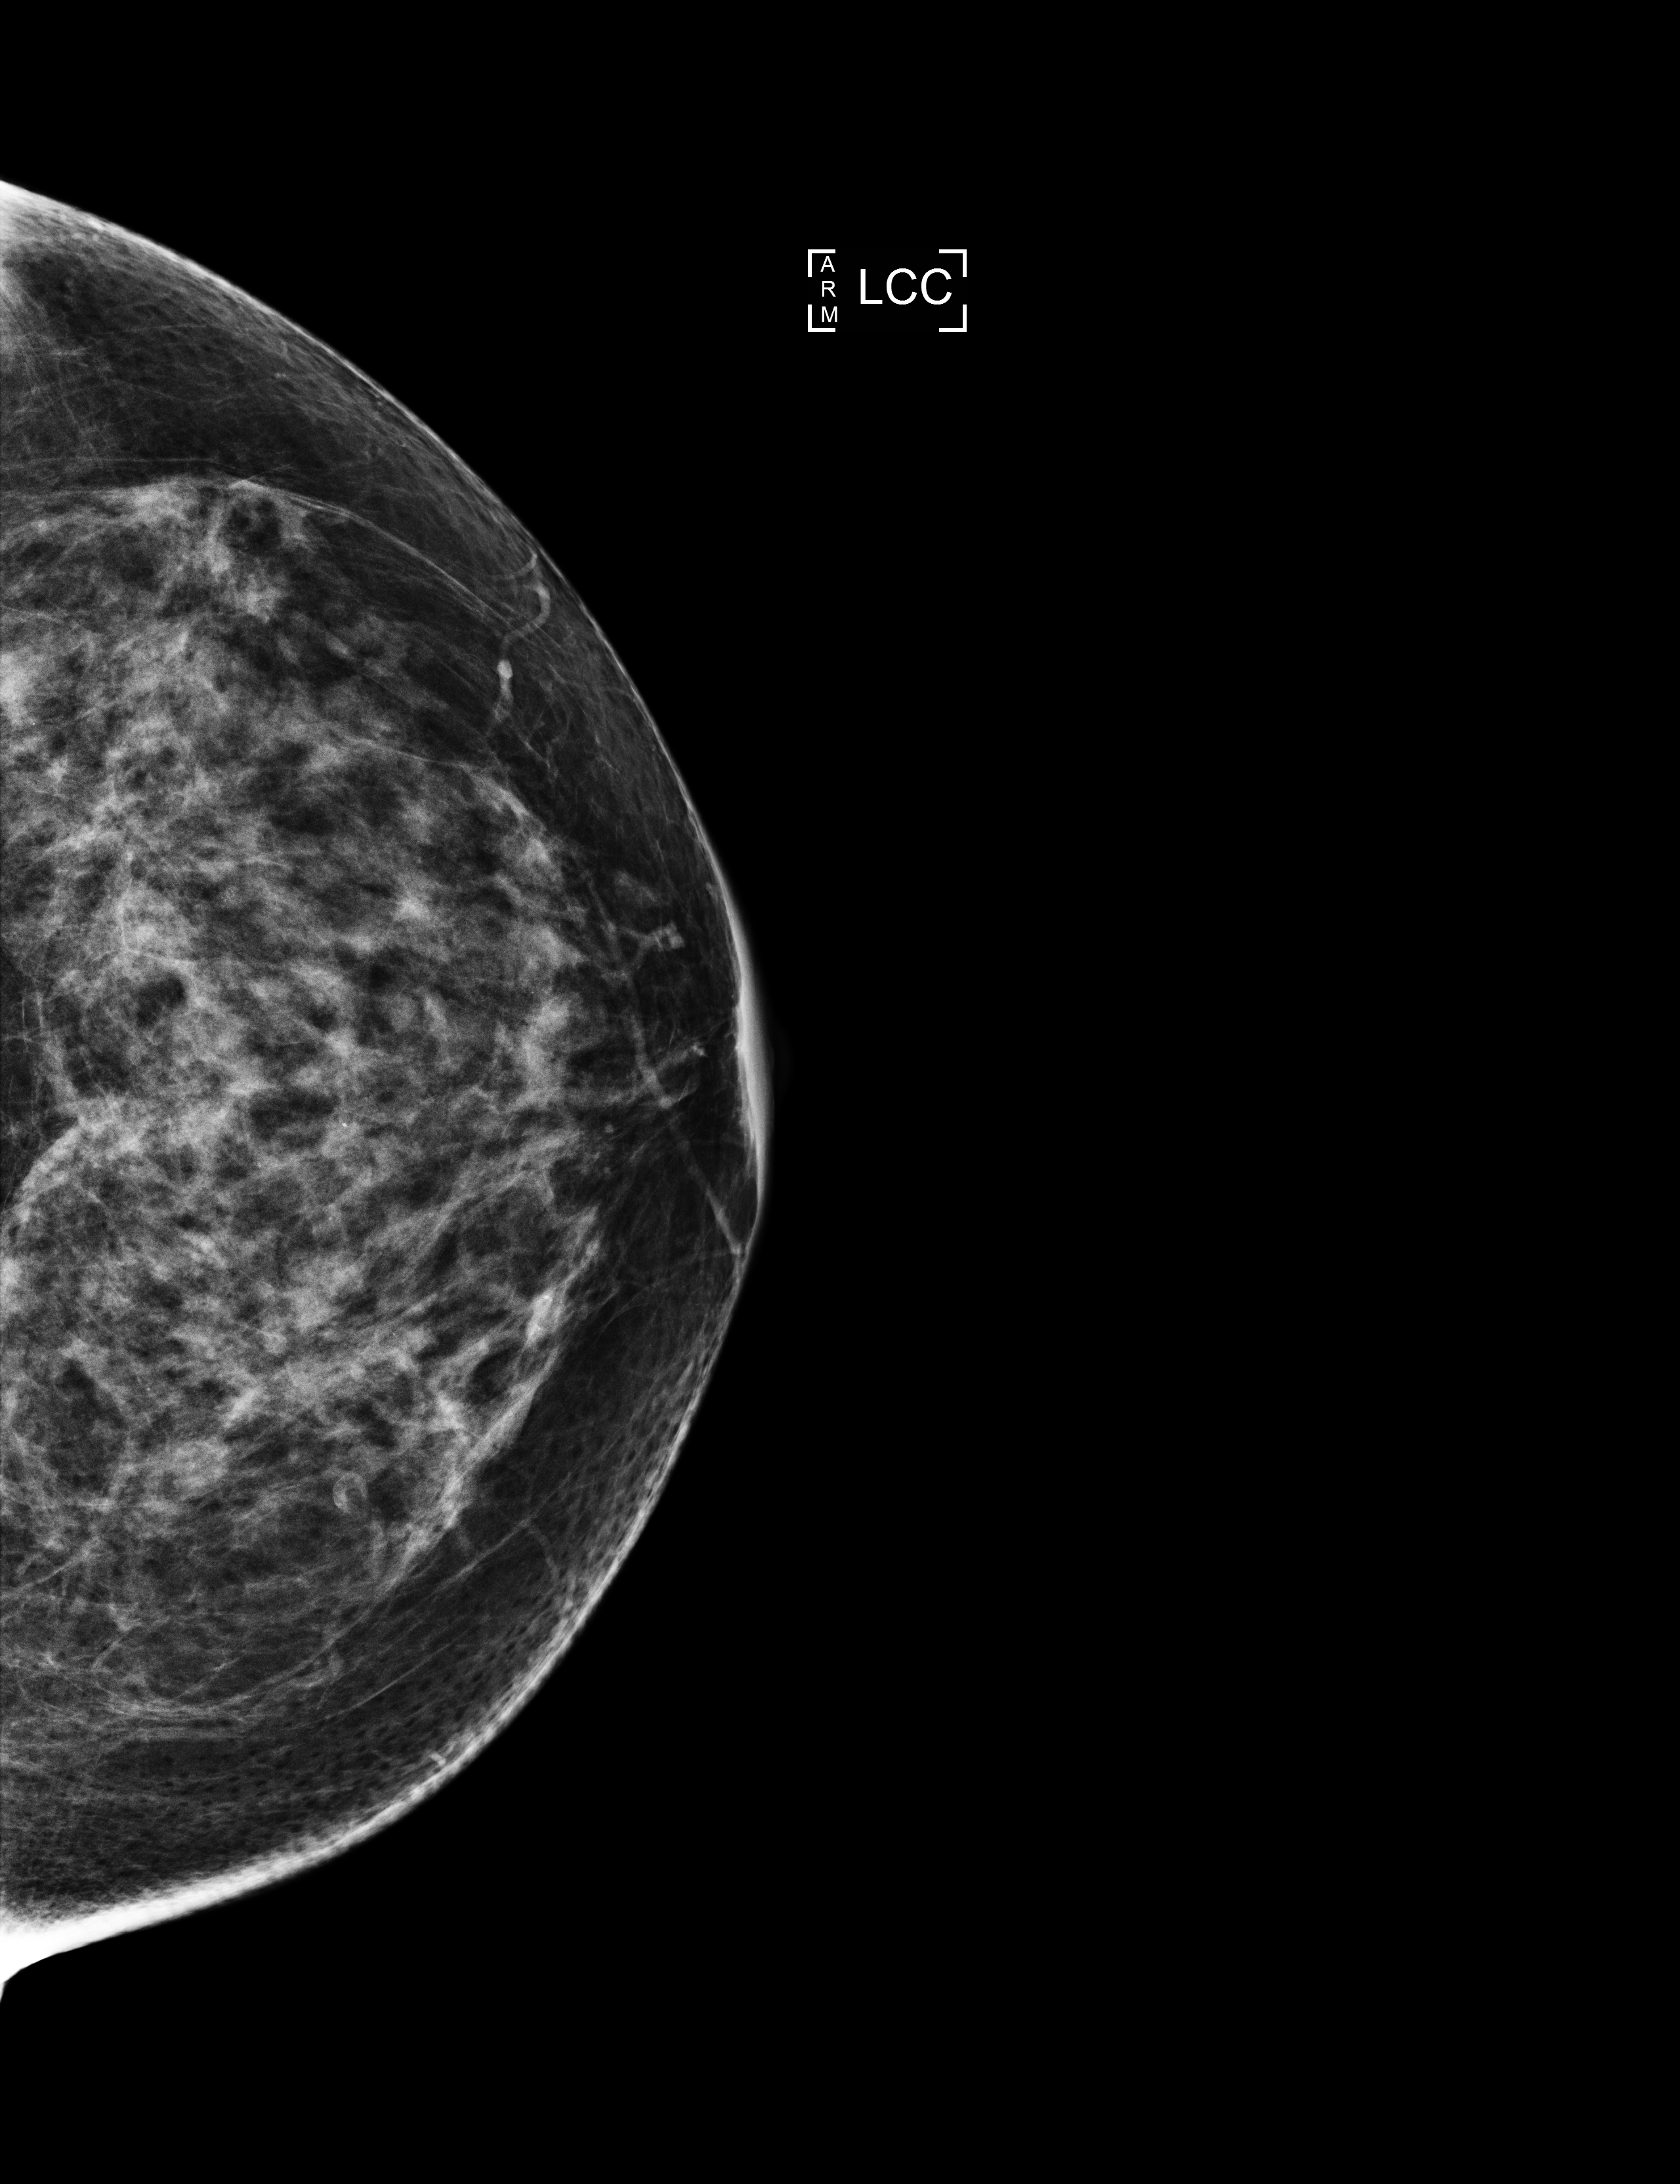
Annual screening mammography examination, system: Selenia Dimensions.
Image type: full-field digital mammogram. Breast: left. Projection: cranio-caudal projection.